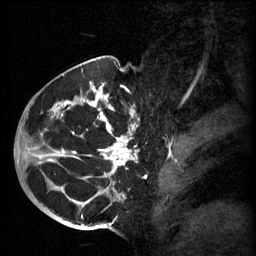
Breast MRI (dynamic contrast-enhanced), one sagittal slice. Position 41 of 60 along the scan axis. 3 images stored at this slice position (order not interpretable as contrast timing). 1.5 T. TE 4.2 ms, TR 11 ms. 2 mm slice thickness. 256 × 256 image matrix, field of view 200 × 200 mm. Female patient, age 51 years.
Annotated regions visible in this slice (semi-automatic segmentation, software-assisted and operator-edited):
- analysis volume of interest (the breast-tissue region the enhancement analysis was run in; not a lesion): bounding box <48,82,161,197> (left, top, right, bottom; pixels)
- tumour enhancement mask (voxels above the 70 % enhancement threshold inside the analysis volume of interest): <48,86,137,197>